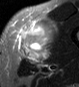
MRI of an extremity soft-tissue mass, one axial slice. Position 28 of 45 along the scan axis. STIR. MR volume resampled by the dataset authors to the PET/CT grid (not the native acquisition matrix). 3.27 mm slice thickness. 79 × 87 image matrix, field of view 77 × 85 mm. Male patient. From the clinical record (not read from this slice): histological type: pleiomorphic leiomyosarcoma; grade: high; site of the primary tumour: left thigh.
Structures marked on this image (expert contour drawn on MRI and transferred to this co-registered scan by the dataset authors):
- gross tumour volume including surrounding oedema: bounding box (x1, y1, x2, y2) in pixels: (18, 18, 57, 62)
- gross tumour volume (mass): (20, 23, 51, 60)